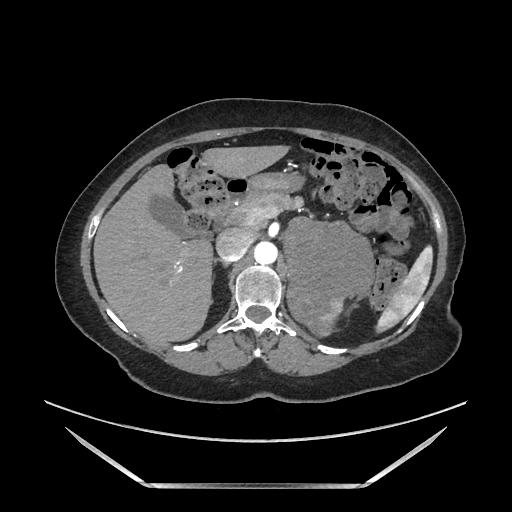
Contrast-enhanced abdominal CT, one axial slice. Slice 110 of 205 in the series (ordered by position). Soft-tissue window (W 400 / L 40 HU). 1.25 mm slice thickness. 512 × 512 image matrix, field of view 440 × 440 mm. Female patient. Case-level facts recorded for this patient, not image findings: diagnosis: adrenocortical carcinoma; tumour side: left adrenal; tumour size at pathology: 12.5 cm; Ki-67 index: 39 %; stage (as recorded): 3.
Annotated regions visible in this slice (semi-automatic segmentation, software-assisted and operator-edited):
- mass: bounding box <285,221,371,333> (left, top, right, bottom; pixels)